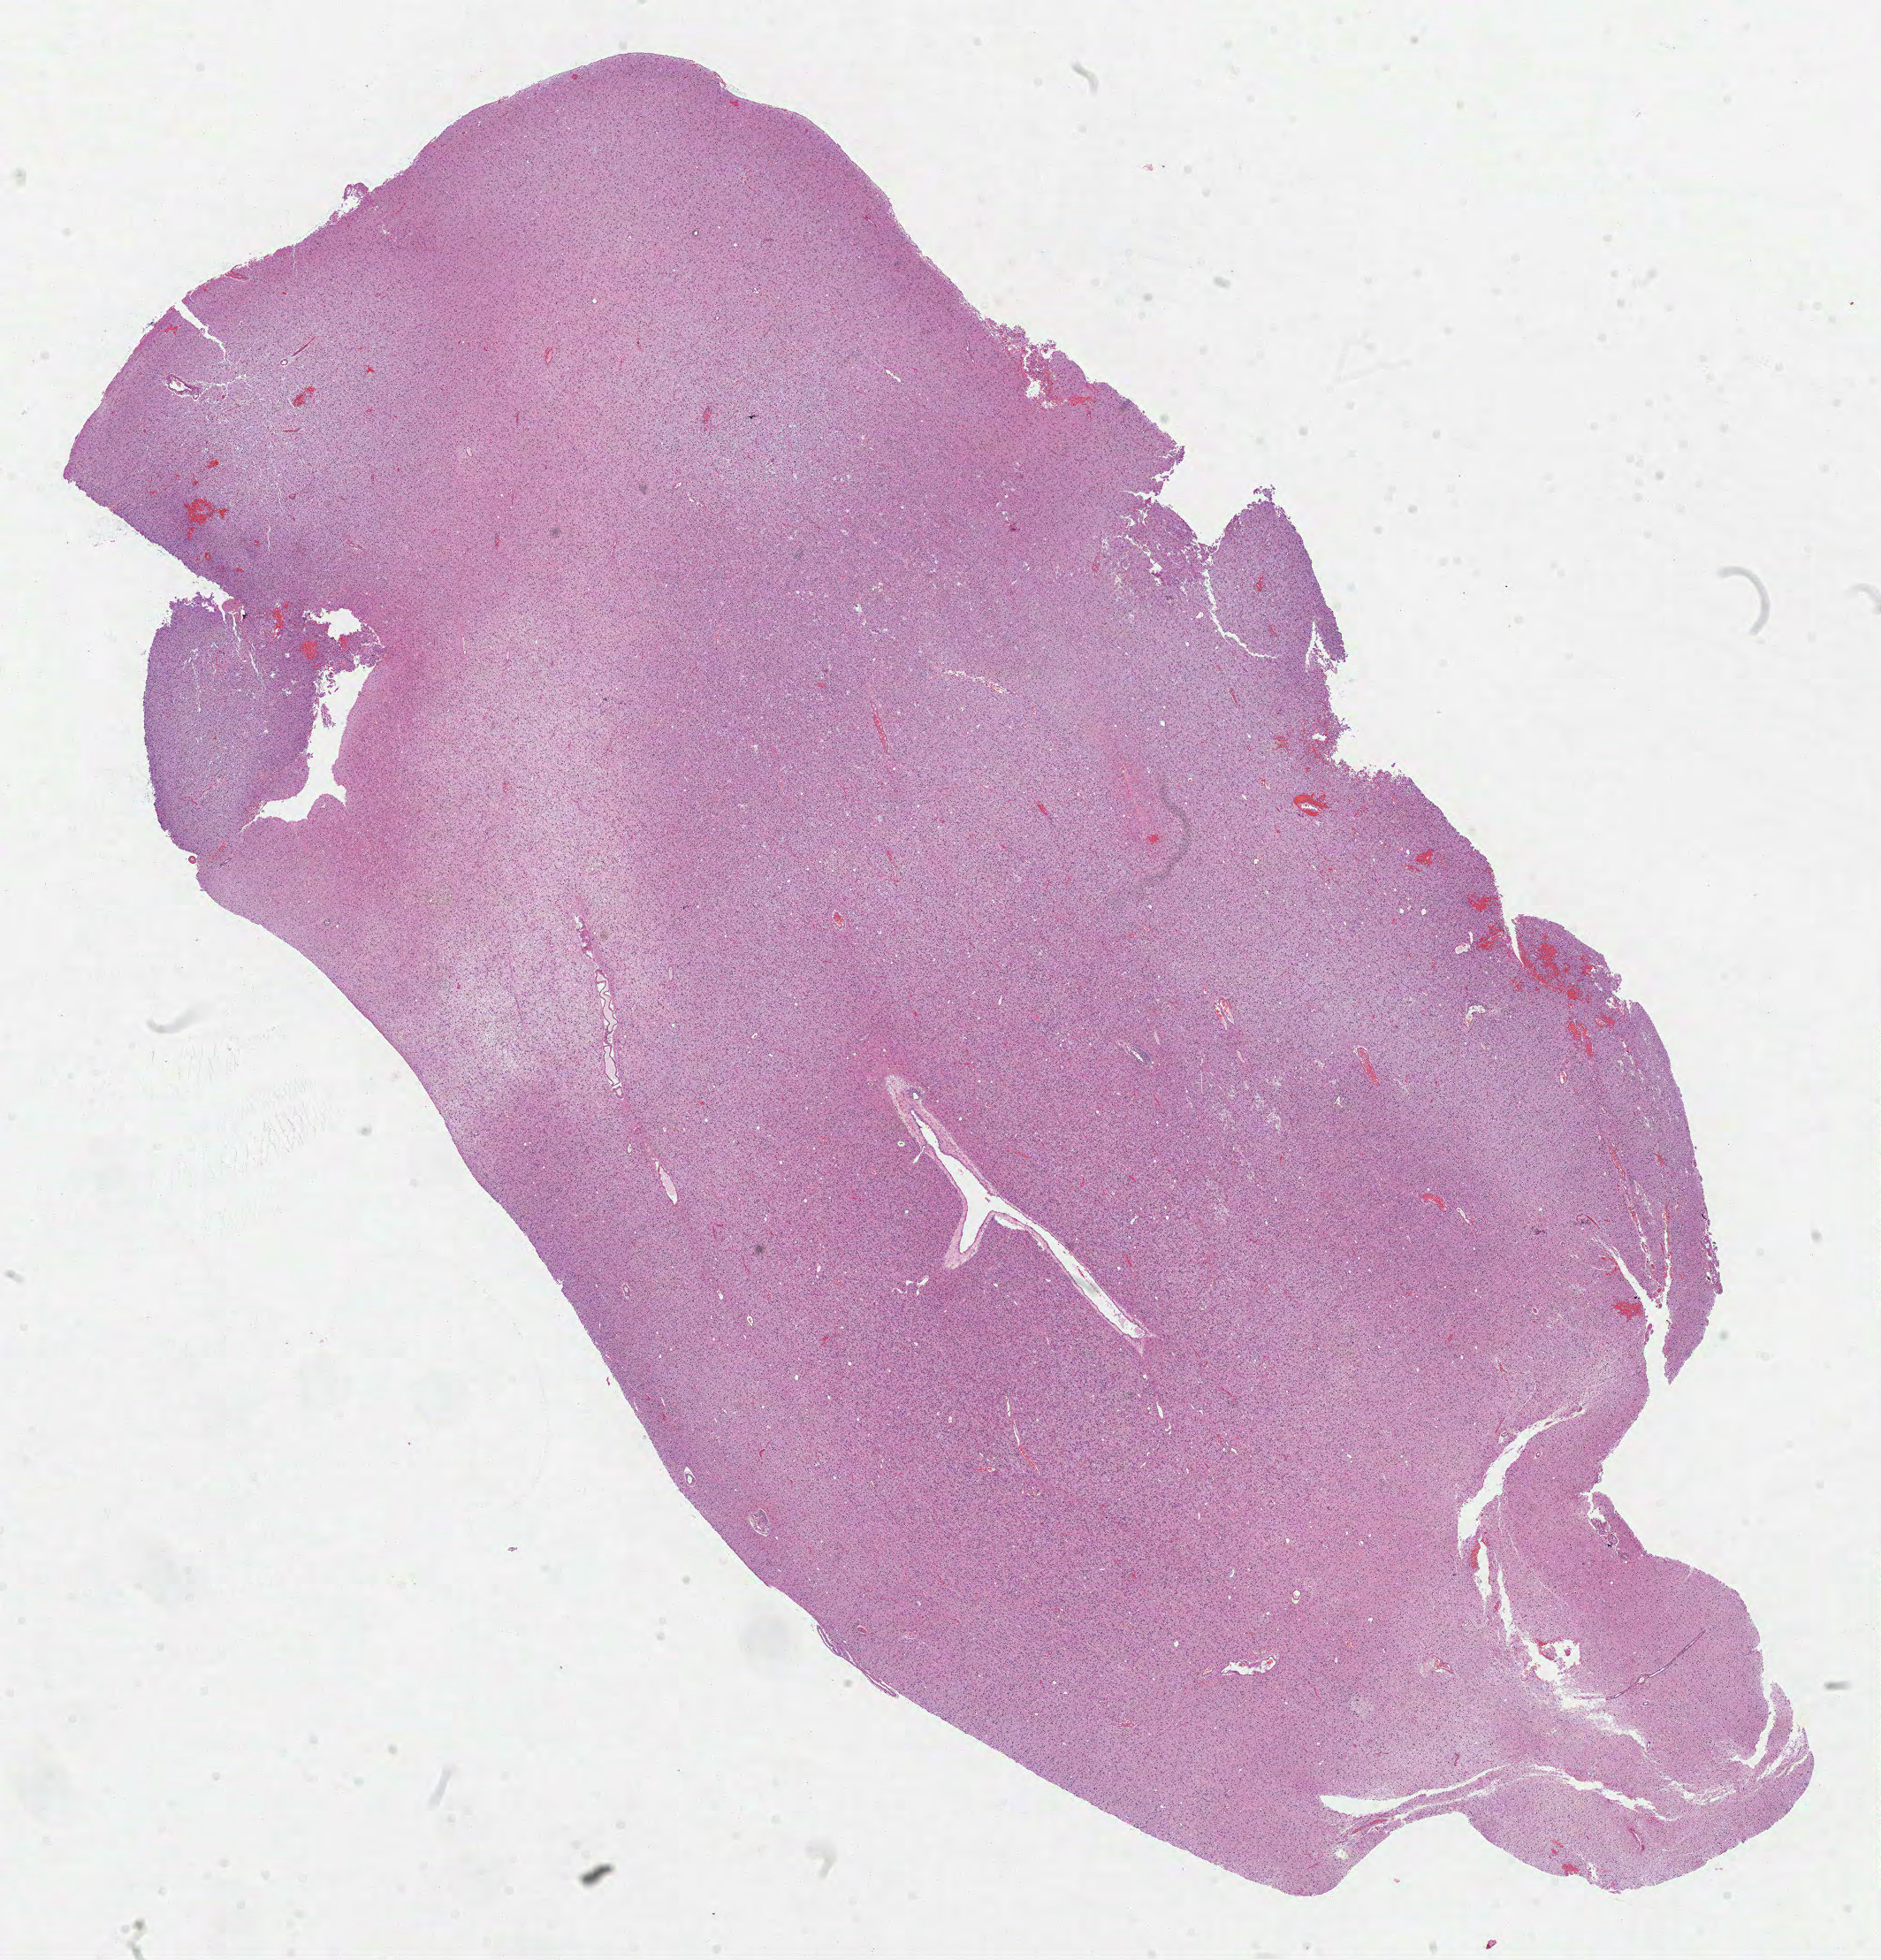
H&E-stained whole-slide image, shown as a low-resolution overview of the whole scanned area (about 17.2 x 17.9 mm, from a 40x scan). FFPE section. Primary tumour sample from the brain. Male, age 25 years at initial diagnosis. Histologic grade: G3 (poorly differentiated).
Histologic diagnosis: Mixed glioma (cerebrum).